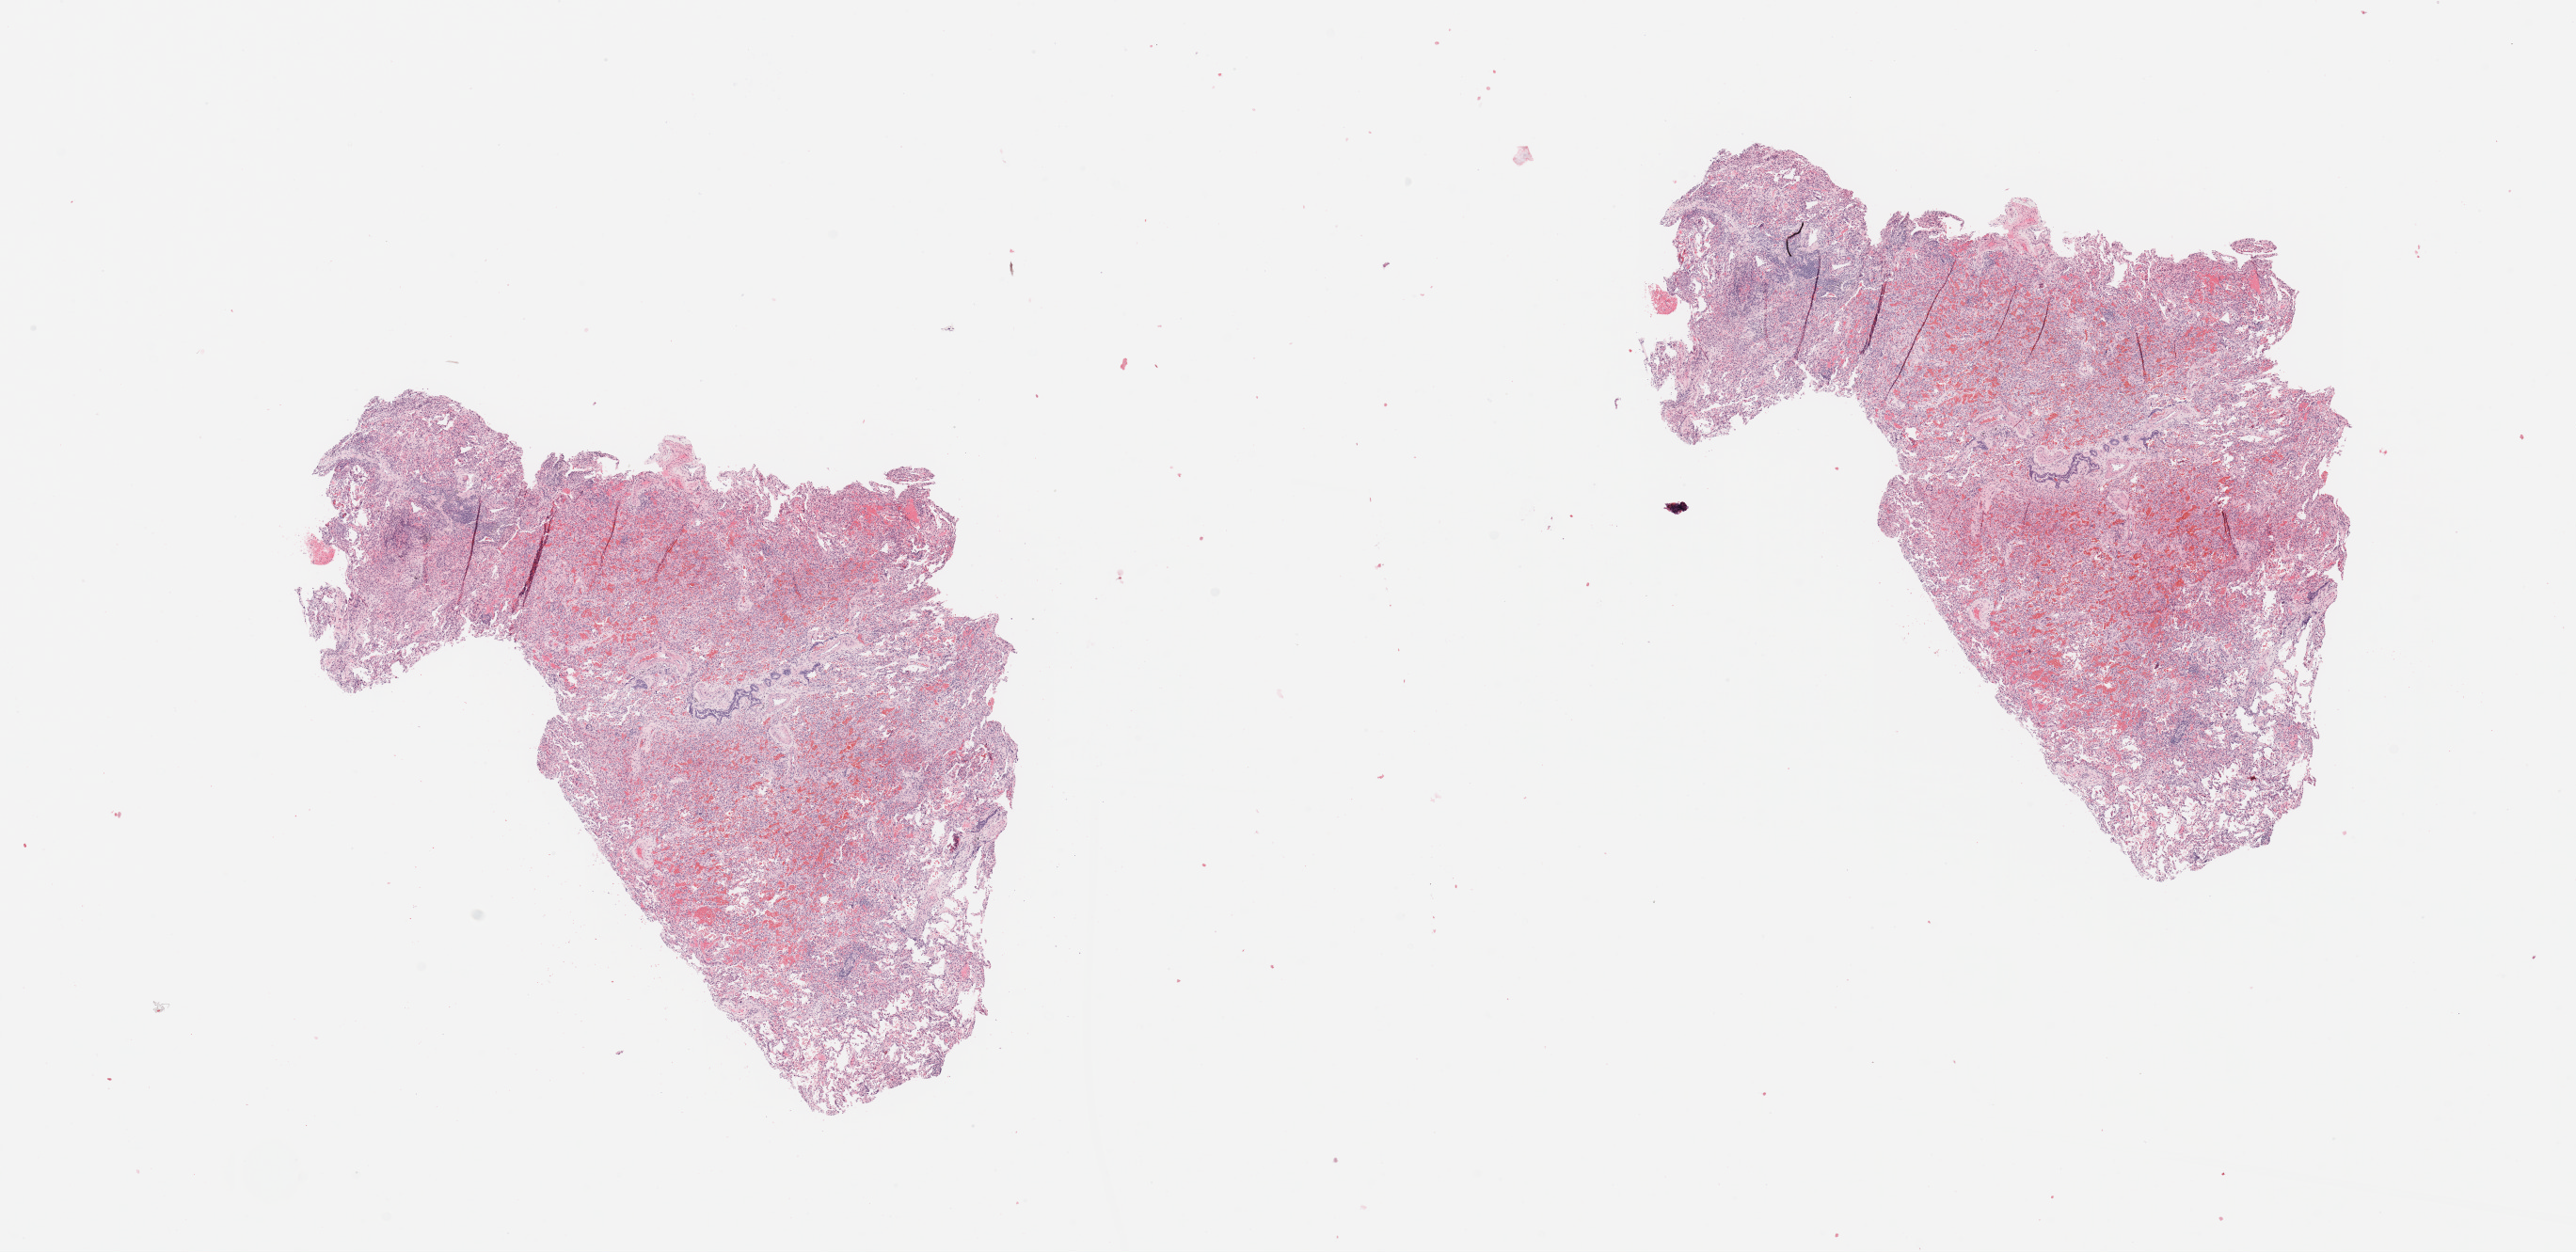
Whole-slide histology image, Hematoxylin and eosin (H&E) stained, low-resolution overview of the scanned area, about 21.7 x 10.5 mm, lung, normal (non-tumour) tissue. Patient: male, age 46 years.
* this section: normal (non-tumour) tissue from the same patient
* patient diagnosis: Adenocarcinoma, NOS